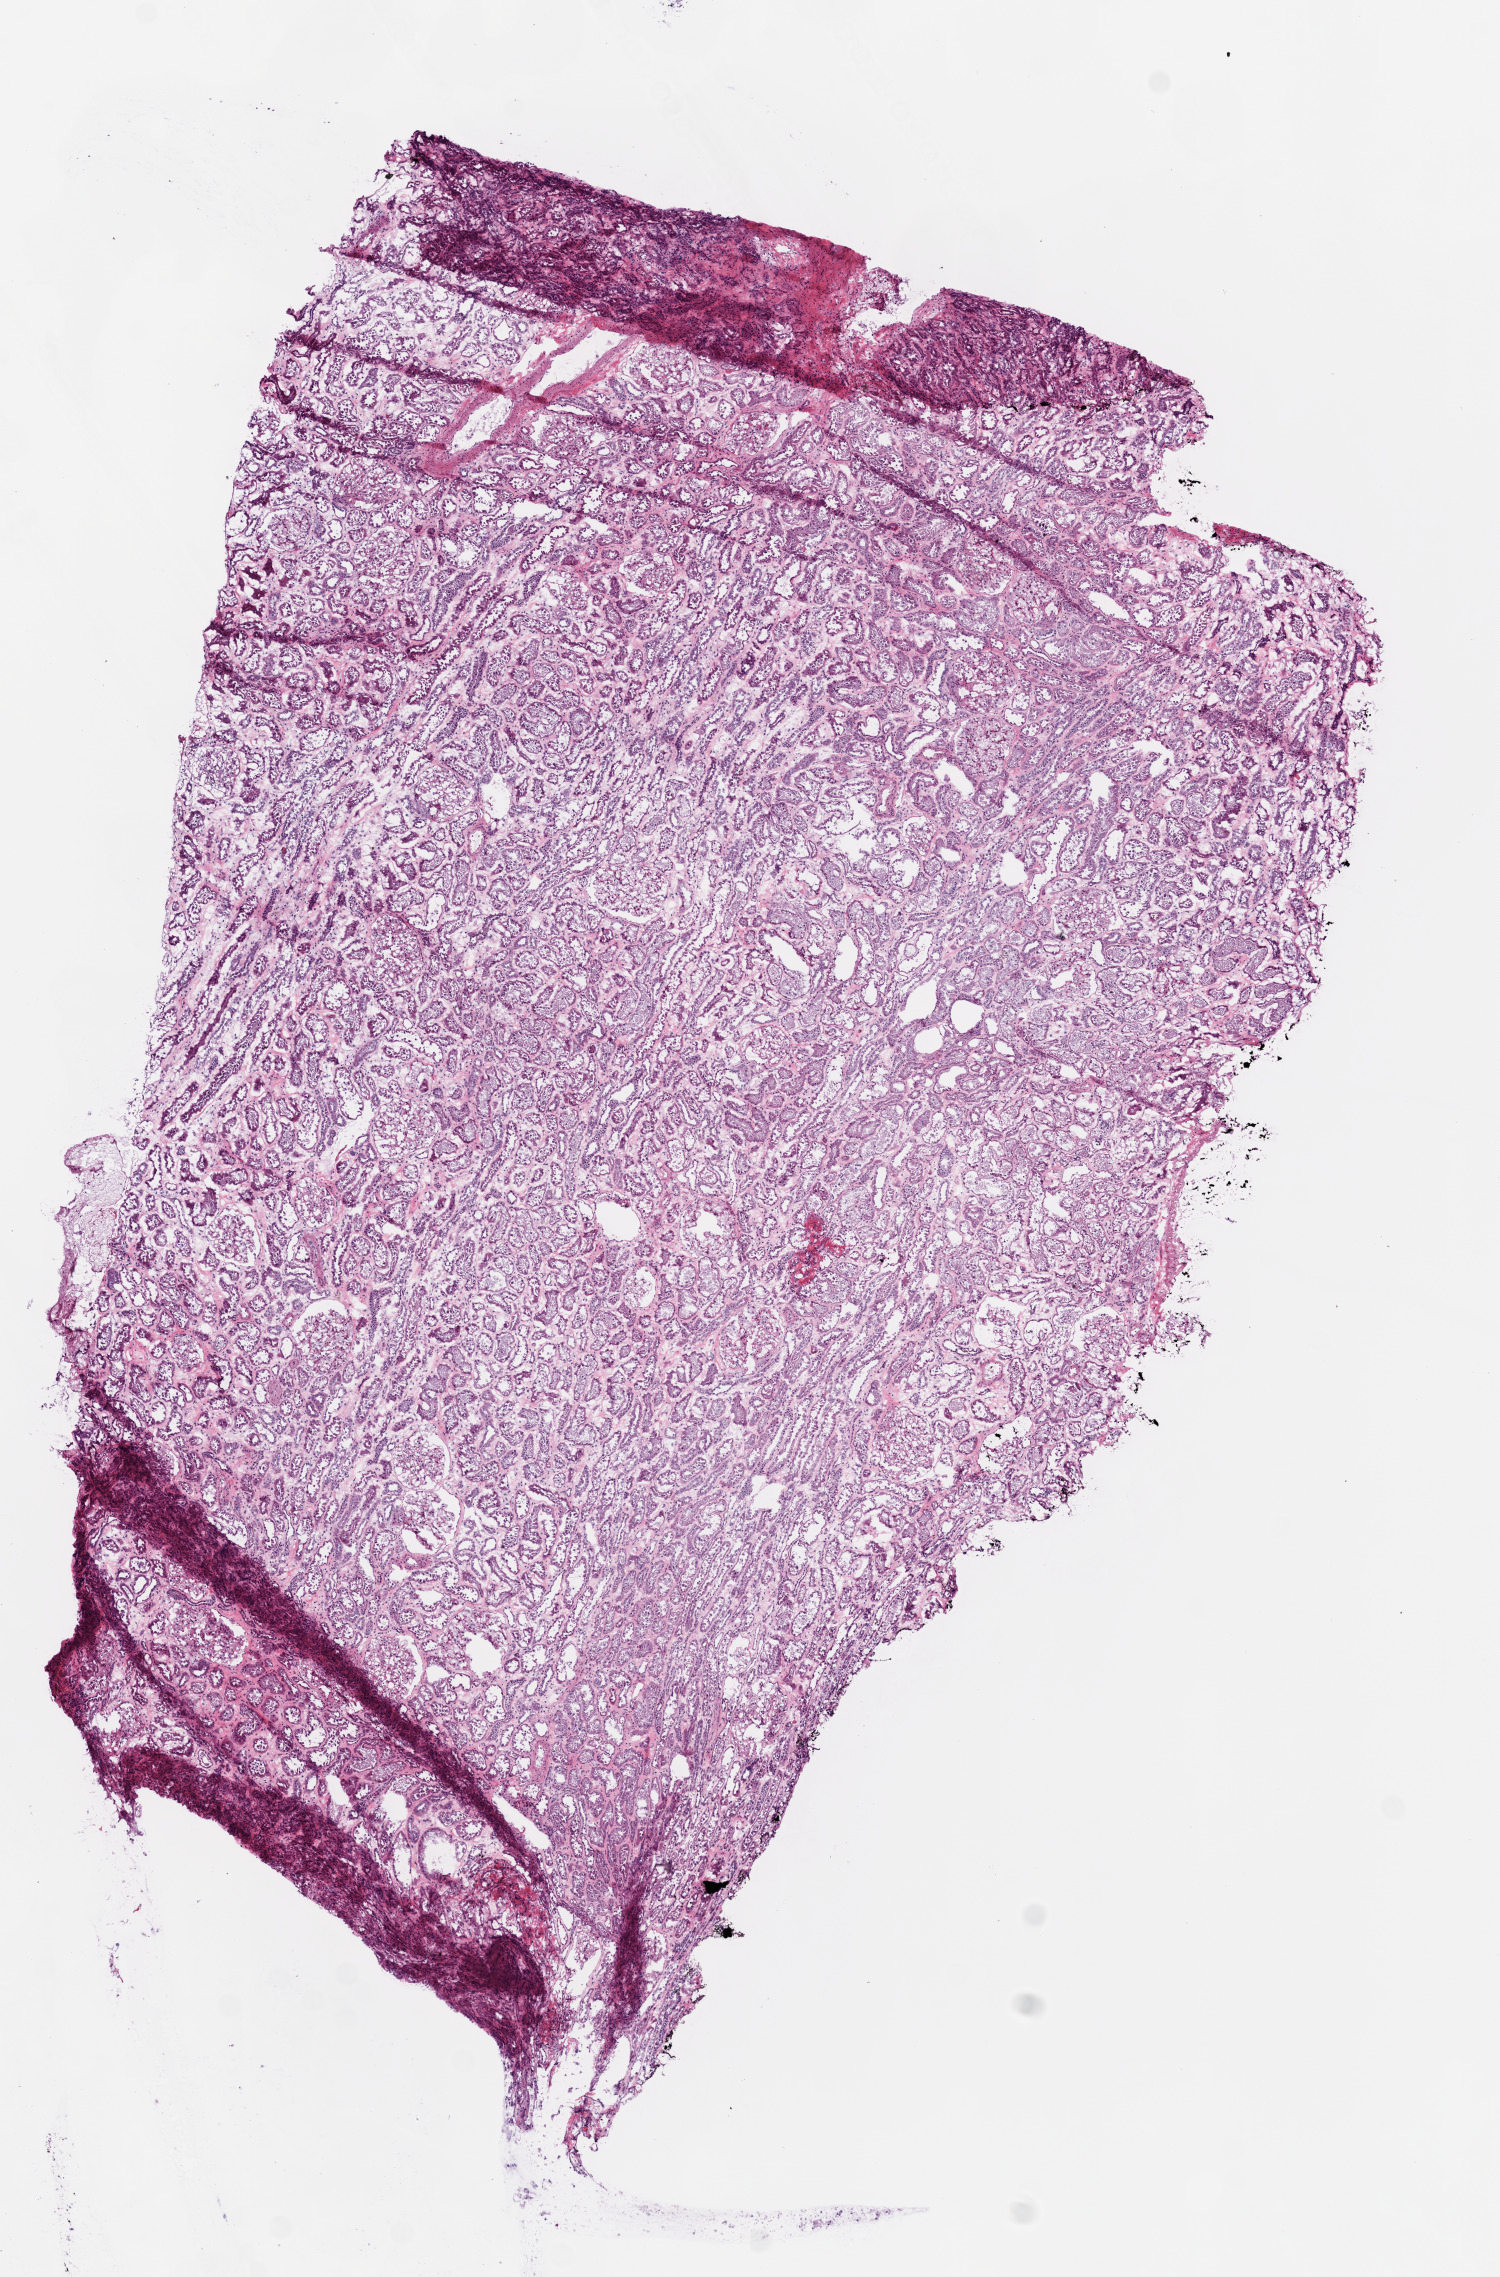
Digitized H&E tissue section (whole slide) — a low-resolution overview of the entire scanned area, about 6.0 x 9.1 mm; frozen section from the top of the tissue portion; sample: solid tissue normal (non-tumour tissue), kidney. Patient: male, age at initial diagnosis 47 years.
This section: solid tissue normal (non-tumour) sample from the same patient. Patient diagnosis: Clear cell adenocarcinoma, NOS.